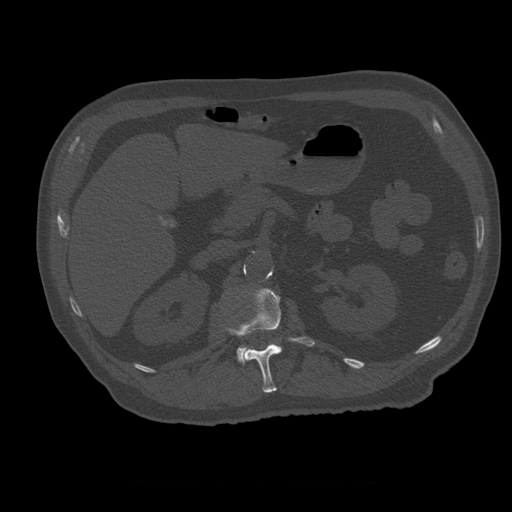
CT including the spine, one axial slice. Slice 232 of 399 in the series (ordered by position). Bone window (W 1800 / L 400 HU). 1.25 mm slice thickness. 512 × 512 image matrix, field of view 407 × 407 mm. Patient age 73 years. From the clinical record (not read from this slice): primary cancer: prostate.
Annotated regions visible in this slice (semi-automatically segmented with operator editing):
- L1 vertebra: bounding box (x1, y1, x2, y2) in pixels: (227, 288, 315, 393)
- L2 vertebra: (237, 347, 248, 363)